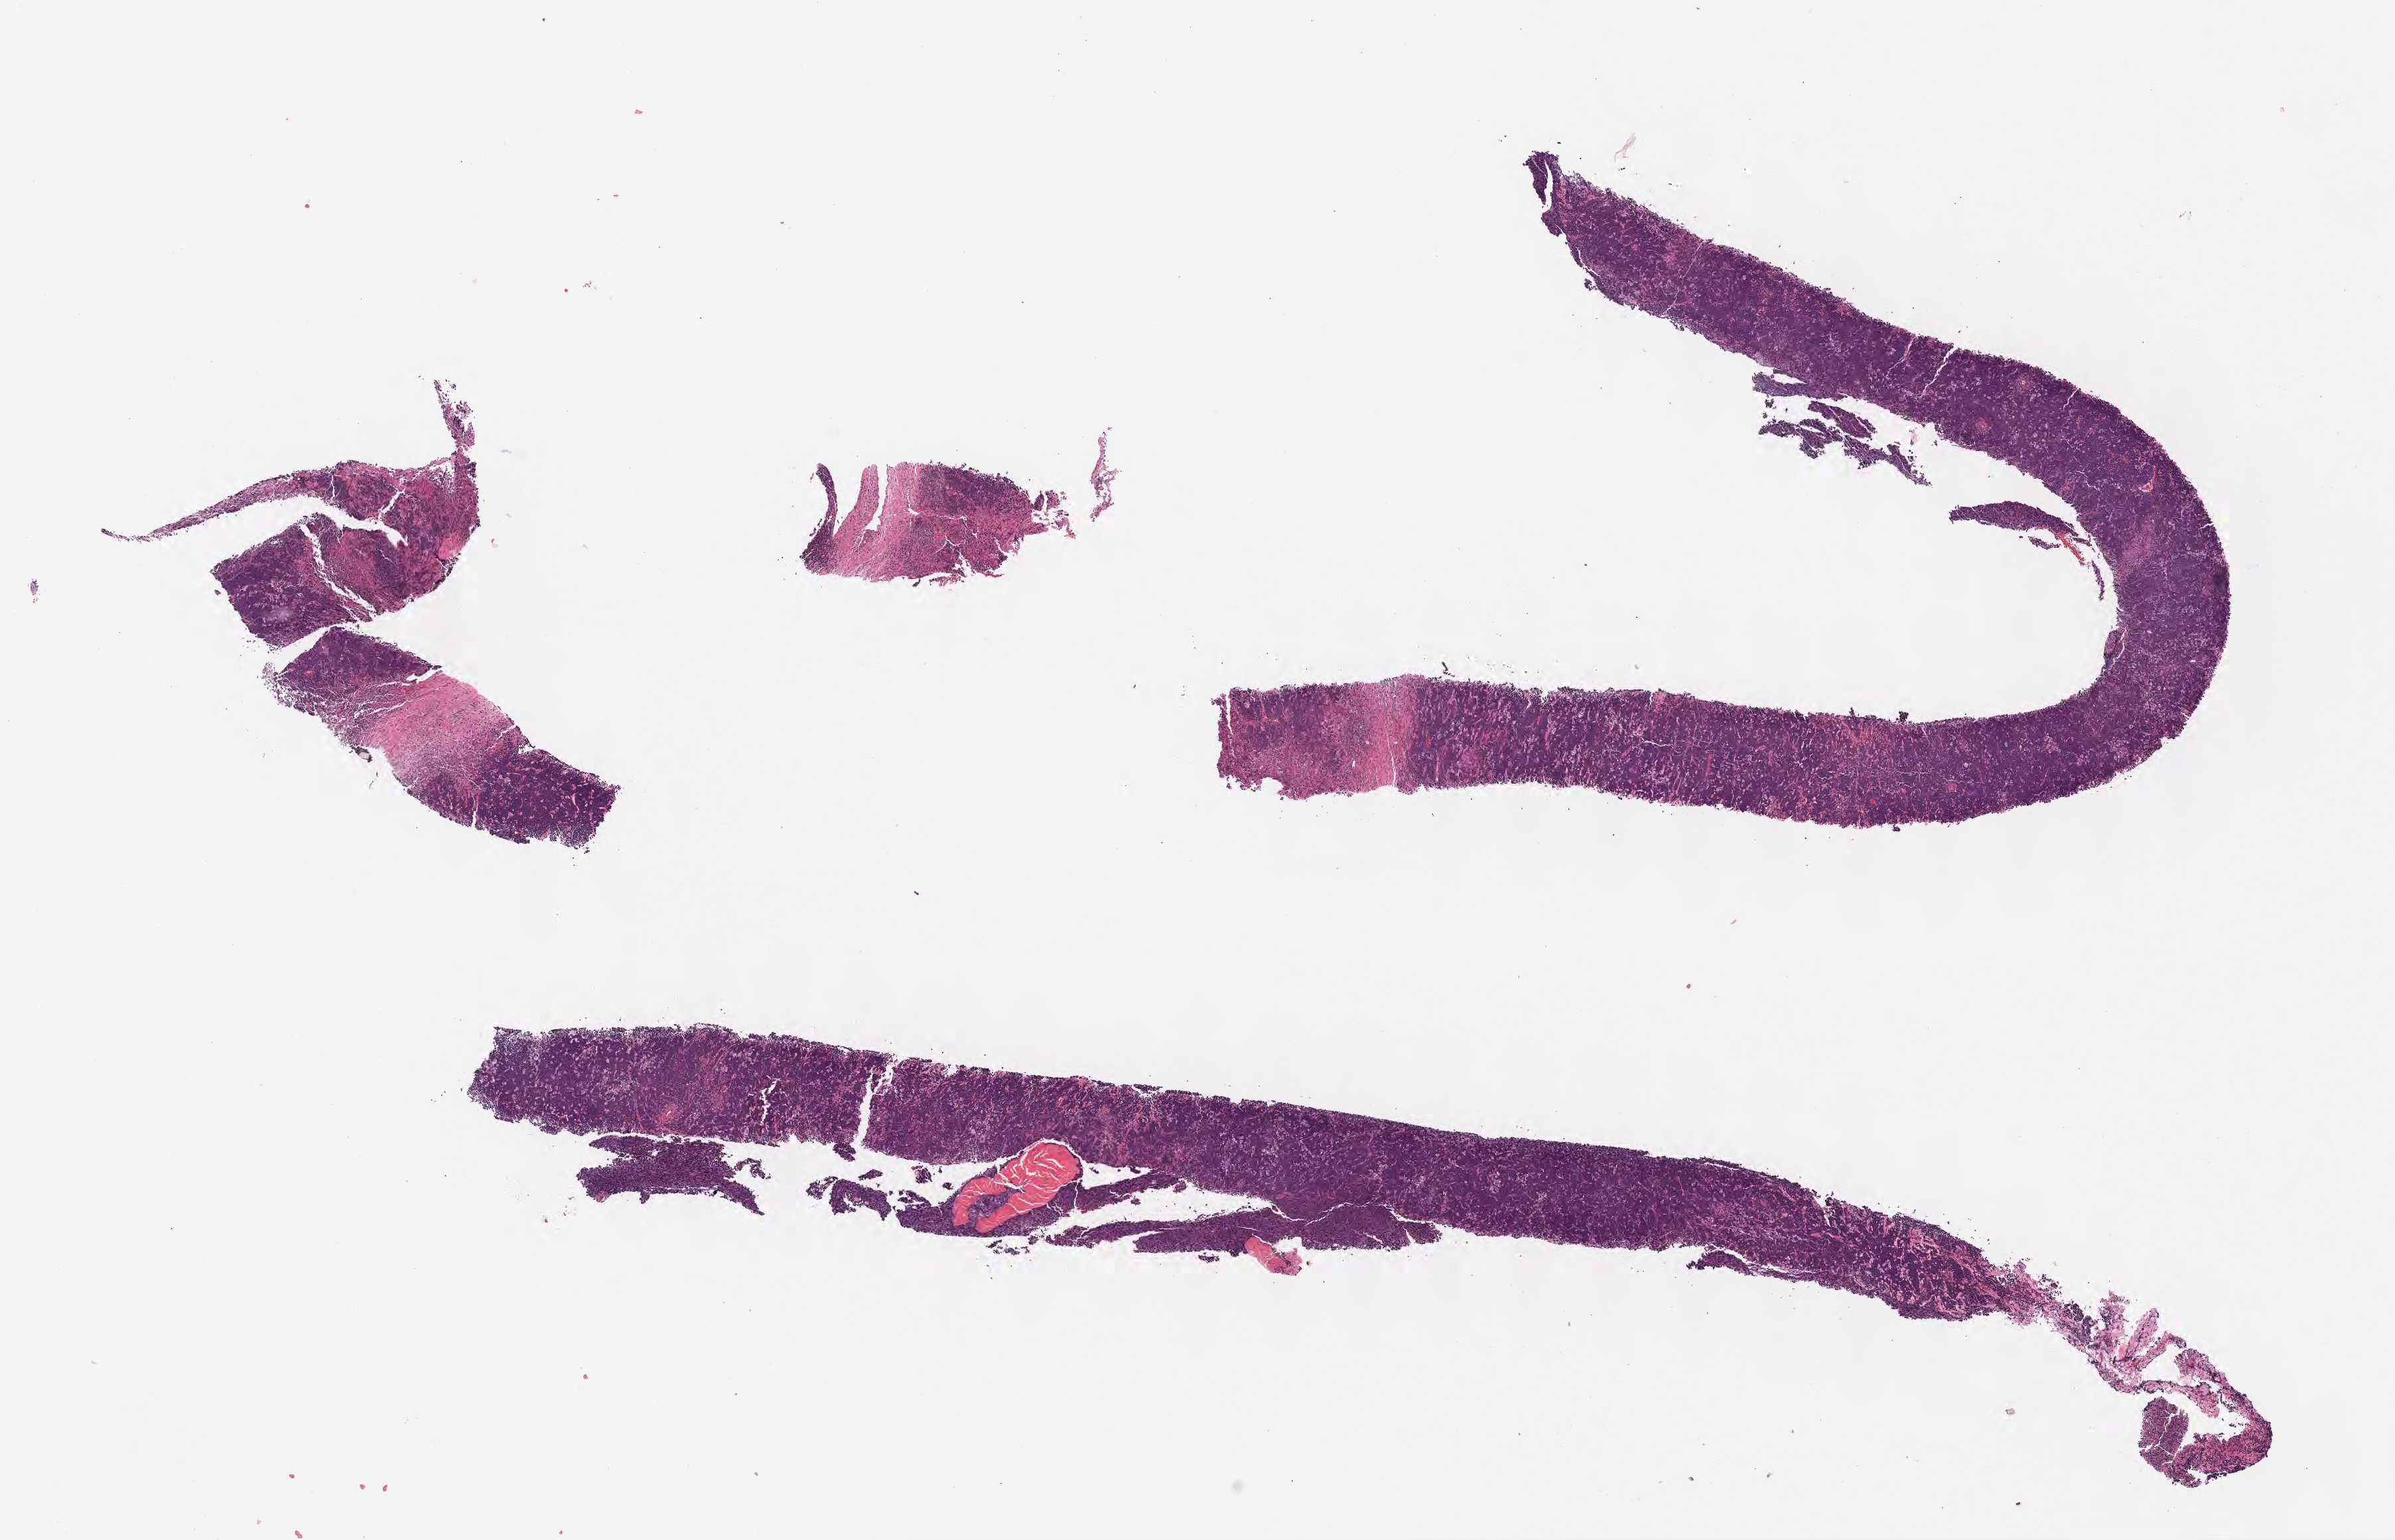
H&E whole-slide image — shown as a low-resolution overview of the whole scanned area (about 14.6 x 9.4 mm). Tumor tissue. Patient male; 55 years old.
* diagnosis: Burkitt lymphoma, NOS